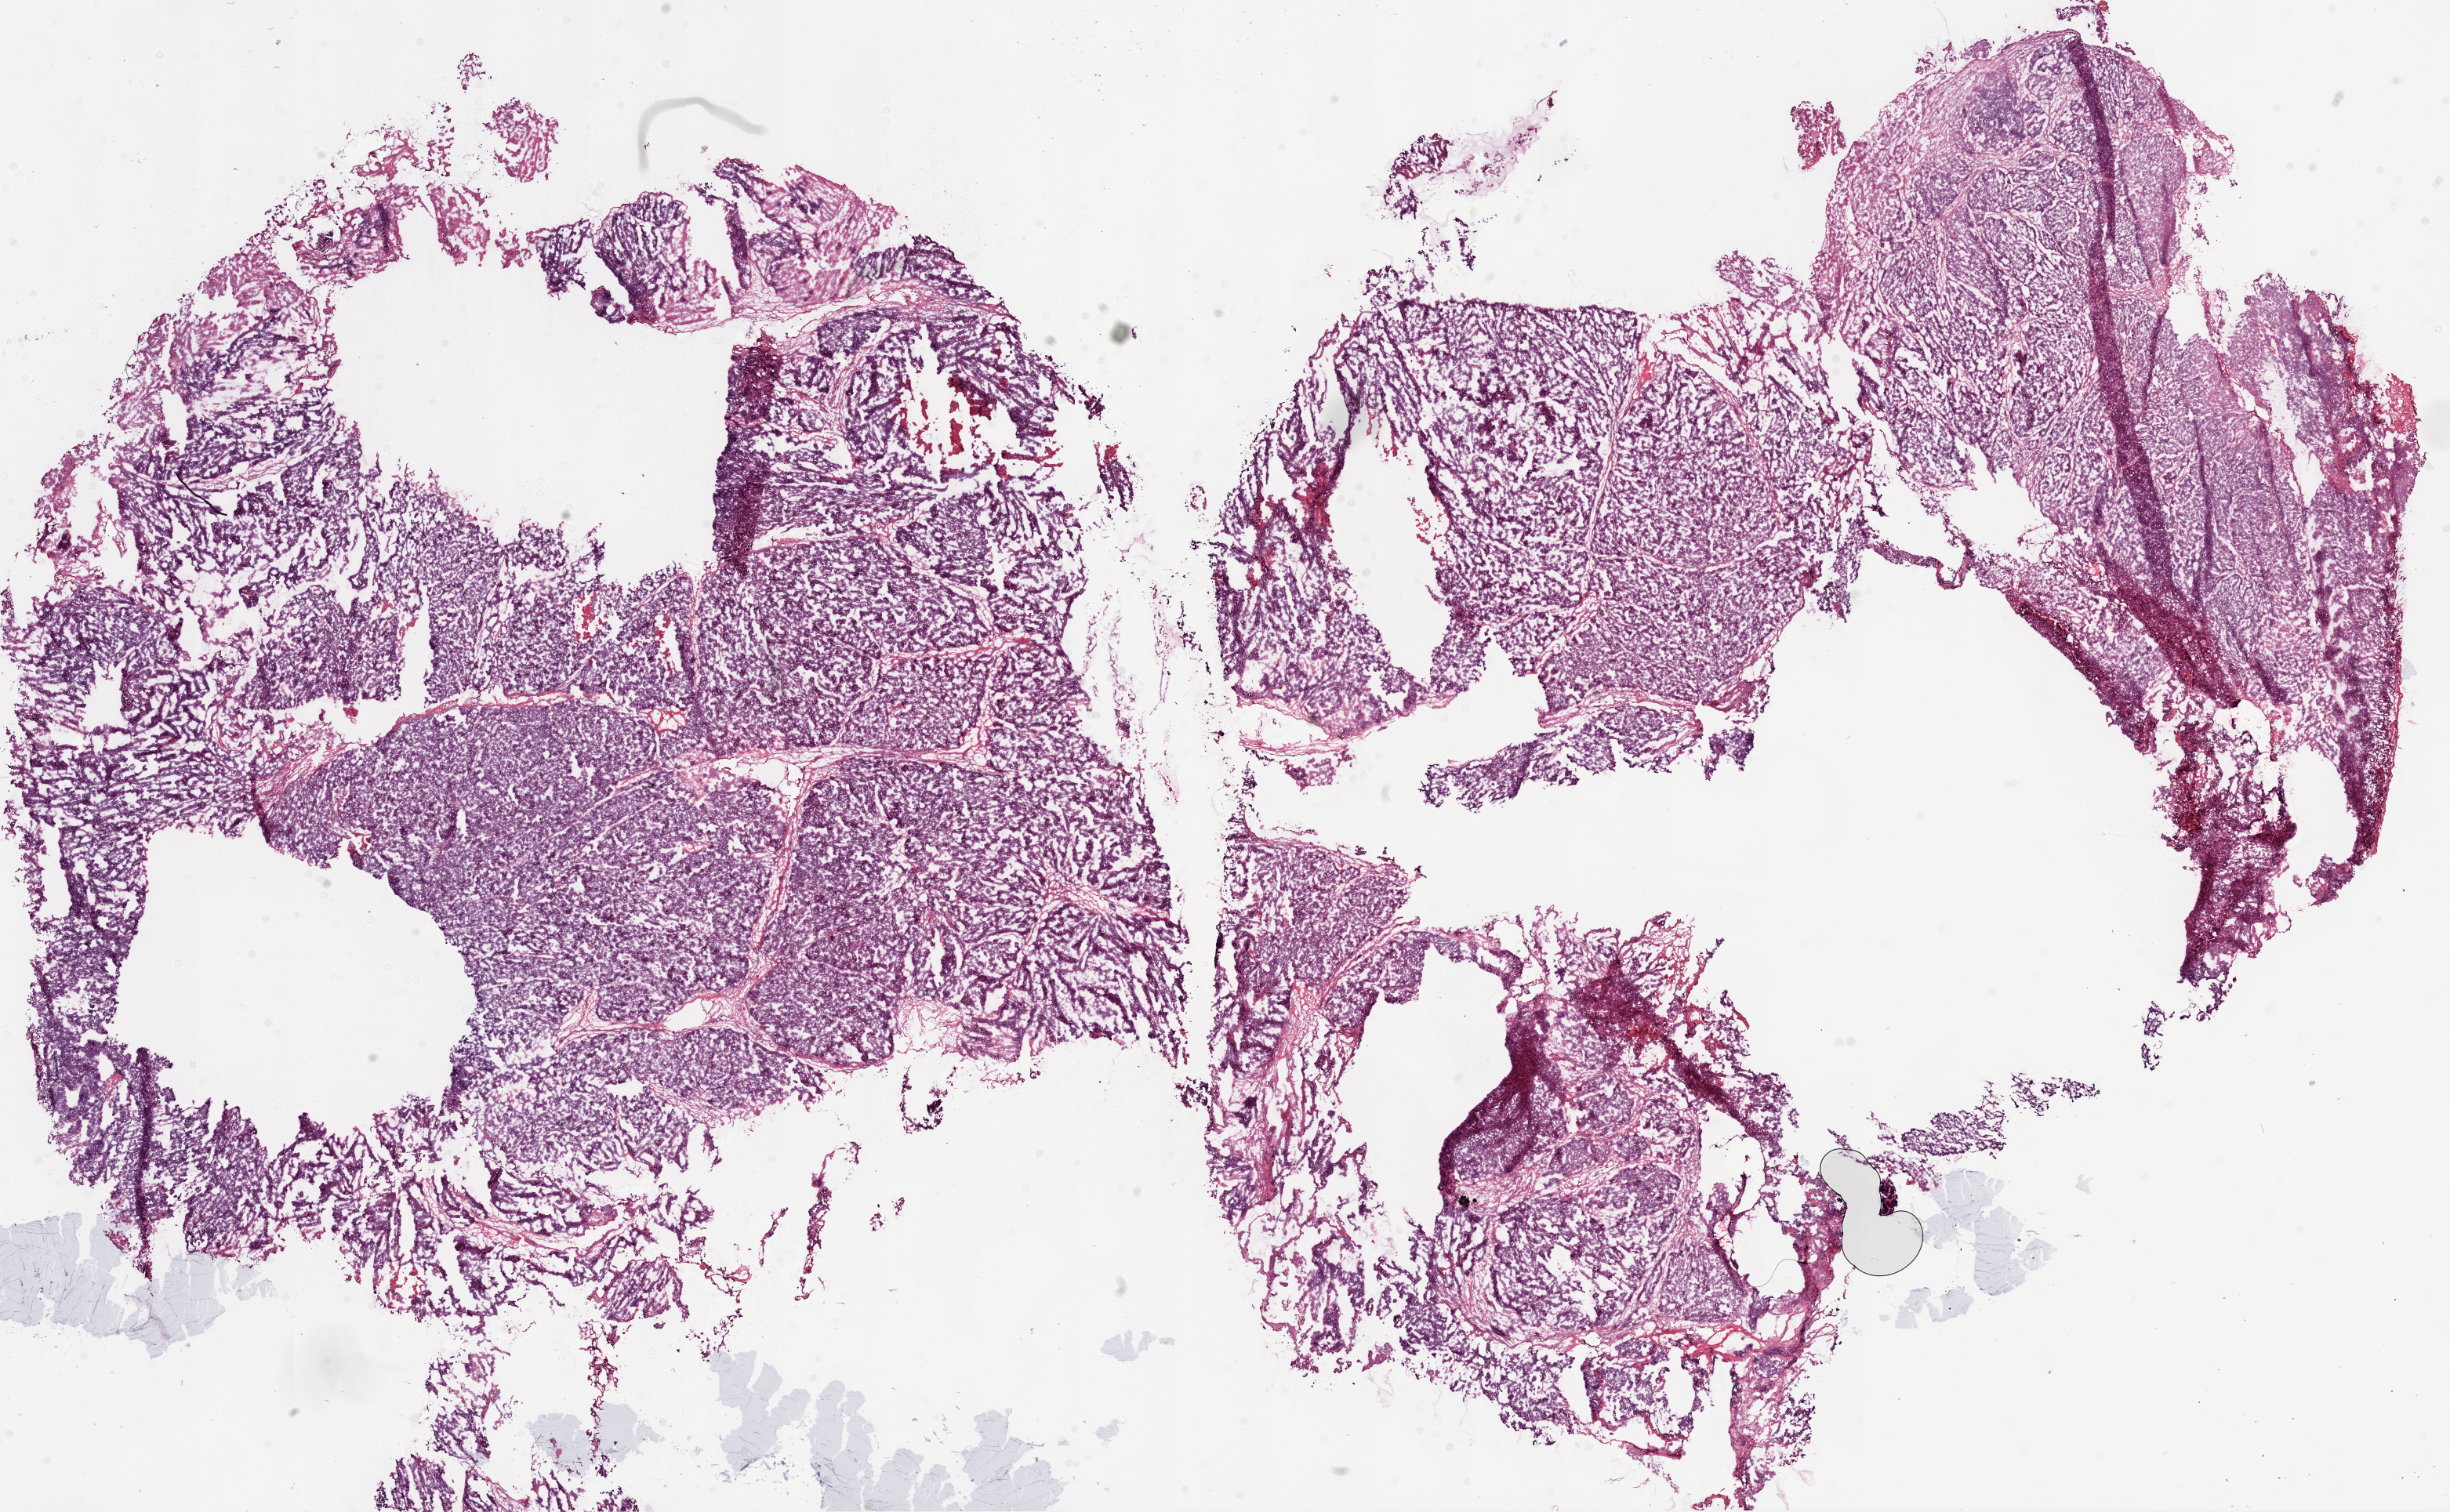
Digitized Hematoxylin and eosin (H&E) stained tissue section (whole slide) — shown as a low-resolution overview of the whole scanned area (about 25.1 x 15.5 mm); frozen section from the bottom of the tissue portion; ovary, primary tumour sample. Female patient; age at initial diagnosis 66 years. Histologic grade: G3 (poorly differentiated). Pathologist review of this section (percent, as recorded): tumour cells 94%, tumour nuclei 99%, normal cells 0%, stromal cells 1%, necrosis 5%.
- histologic diagnosis: Serous cystadenocarcinoma, NOS
- FIGO stage: IIIC